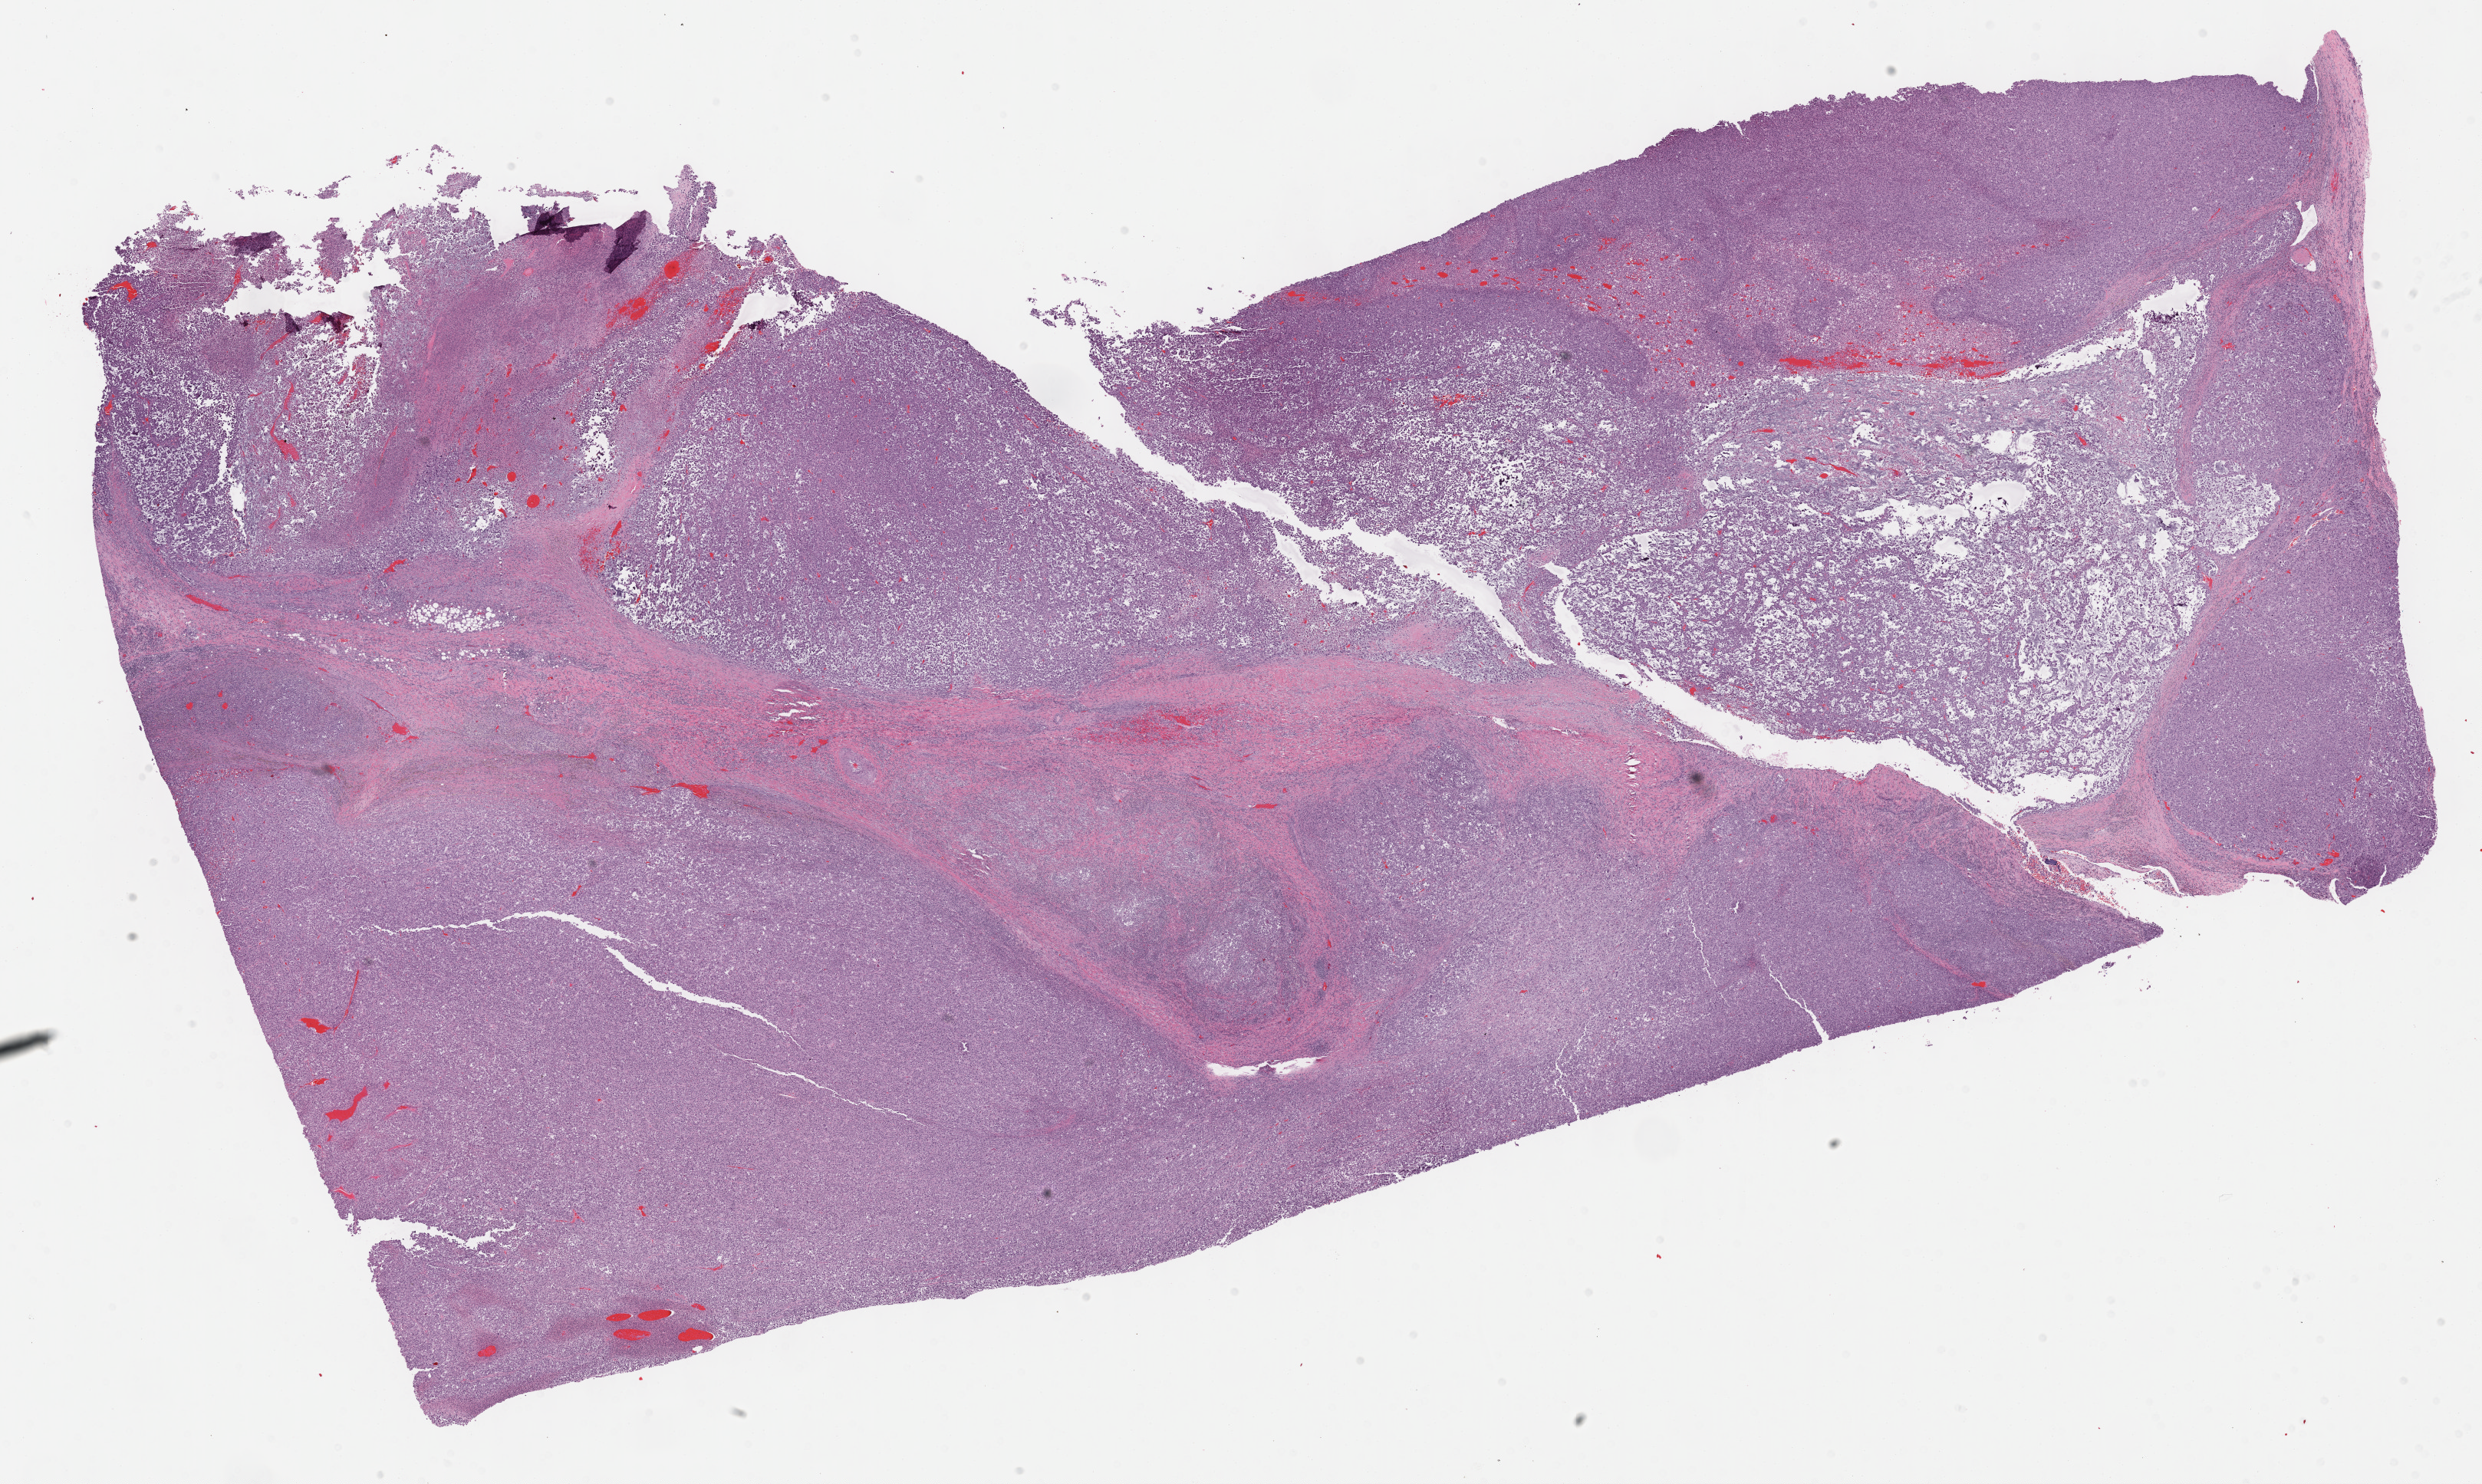
Whole-slide histology image, Hematoxylin and eosin (H&E) stained — low-resolution overview of the scanned area, about 26.2 x 15.7 mm. FFPE section. Connective, subcutaneous and other soft tissues, primary tumour sample. Female patient; age at initial diagnosis 73 years.
Pathologic diagnosis: Undifferentiated sarcoma (connective, subcutaneous and other soft tissues of lower limb and hip).